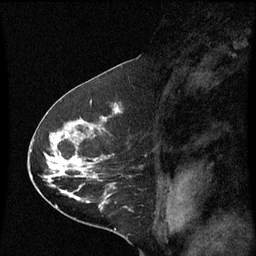
Breast MRI (dynamic contrast-enhanced), one sagittal slice; position 35 of 60 along the scan axis; dynamic contrast-enhanced series, image 2 of 3 at this slice position (ordered by acquisition); 1.5 T; TE 4.2 ms, TR 8.9 ms; 256 × 256 image matrix. Patient: female, 53 years. From the clinical record (not read from this slice): setting: breast cancer imaged before/during neoadjuvant chemotherapy; receptor status: HR-positive, HER2-negative.
Annotated regions visible in this slice (semi-automatic segmentation, software-assisted and operator-edited):
- analysis volume of interest (the breast-tissue region the enhancement analysis was run in; not a lesion): box from (x=32, y=100) to (x=127, y=221) px
- tumour enhancement mask (voxels above the 70 % enhancement threshold inside the analysis volume of interest): (x=48, y=154)–(x=95, y=197)